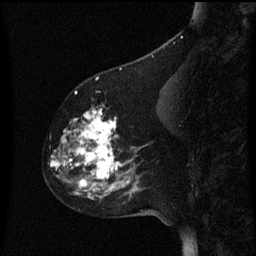
Breast MRI (dynamic contrast-enhanced), one sagittal slice; slice 24 of 60 in the series (ordered by position); dynamic contrast-enhanced series, image 2 of 3 at this slice position (ordered by acquisition); 1.5 T; TE 4.2 ms, TR 8 ms; 2 mm slice thickness; 256 × 256 image matrix, field of view 200 × 200 mm. Female patient, age 60 years.
Structures marked on this image (semi-automatically segmented with operator editing):
- analysis volume of interest (the breast-tissue region the enhancement analysis was run in; not a lesion): bounding box <51,108,149,197> (left, top, right, bottom; pixels)
- tumour enhancement mask (voxels above the 70 % enhancement threshold inside the analysis volume of interest): <51,108,130,197>